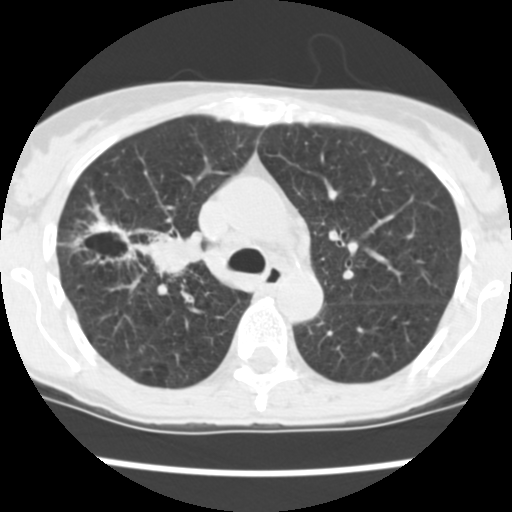
Low-dose screening chest CT, one axial slice; slice 167 of 252 in the series (ordered by position); reconstruction kernel STANDARD; 120 kVp; lung window (W 1500 / L -600 HU); 512 × 512 image matrix.
Structures marked on this image (outlined manually by an expert reader):
- lesion 2 (tumor, lower lobe of right lung): bounding box [x1, y1, x2, y2] px = [70, 214, 204, 277]